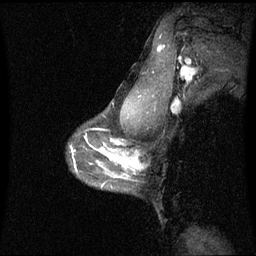
Breast MRI (dynamic contrast-enhanced), one sagittal slice. Position 50 of 60 along the scan axis. Dynamic contrast-enhanced series, image 2 of 3 at this slice position (ordered by acquisition). 1.5 T. TE 4.2 ms, TR 8.9 ms. 2 mm slice thickness. 256 × 256 image matrix, field of view 230 × 230 mm. Female patient, age 42 years. From the clinical record (not read from this slice): setting: breast cancer imaged before/during neoadjuvant chemotherapy; receptor status: triple-negative.
Structures marked on this image (semi-automatically segmented with operator editing):
- analysis volume of interest (the breast-tissue region the enhancement analysis was run in; not a lesion): bounding box <114,150,138,180> (left, top, right, bottom; pixels)
- tumour enhancement mask (voxels above the 70 % enhancement threshold inside the analysis volume of interest): <126,158,138,168>